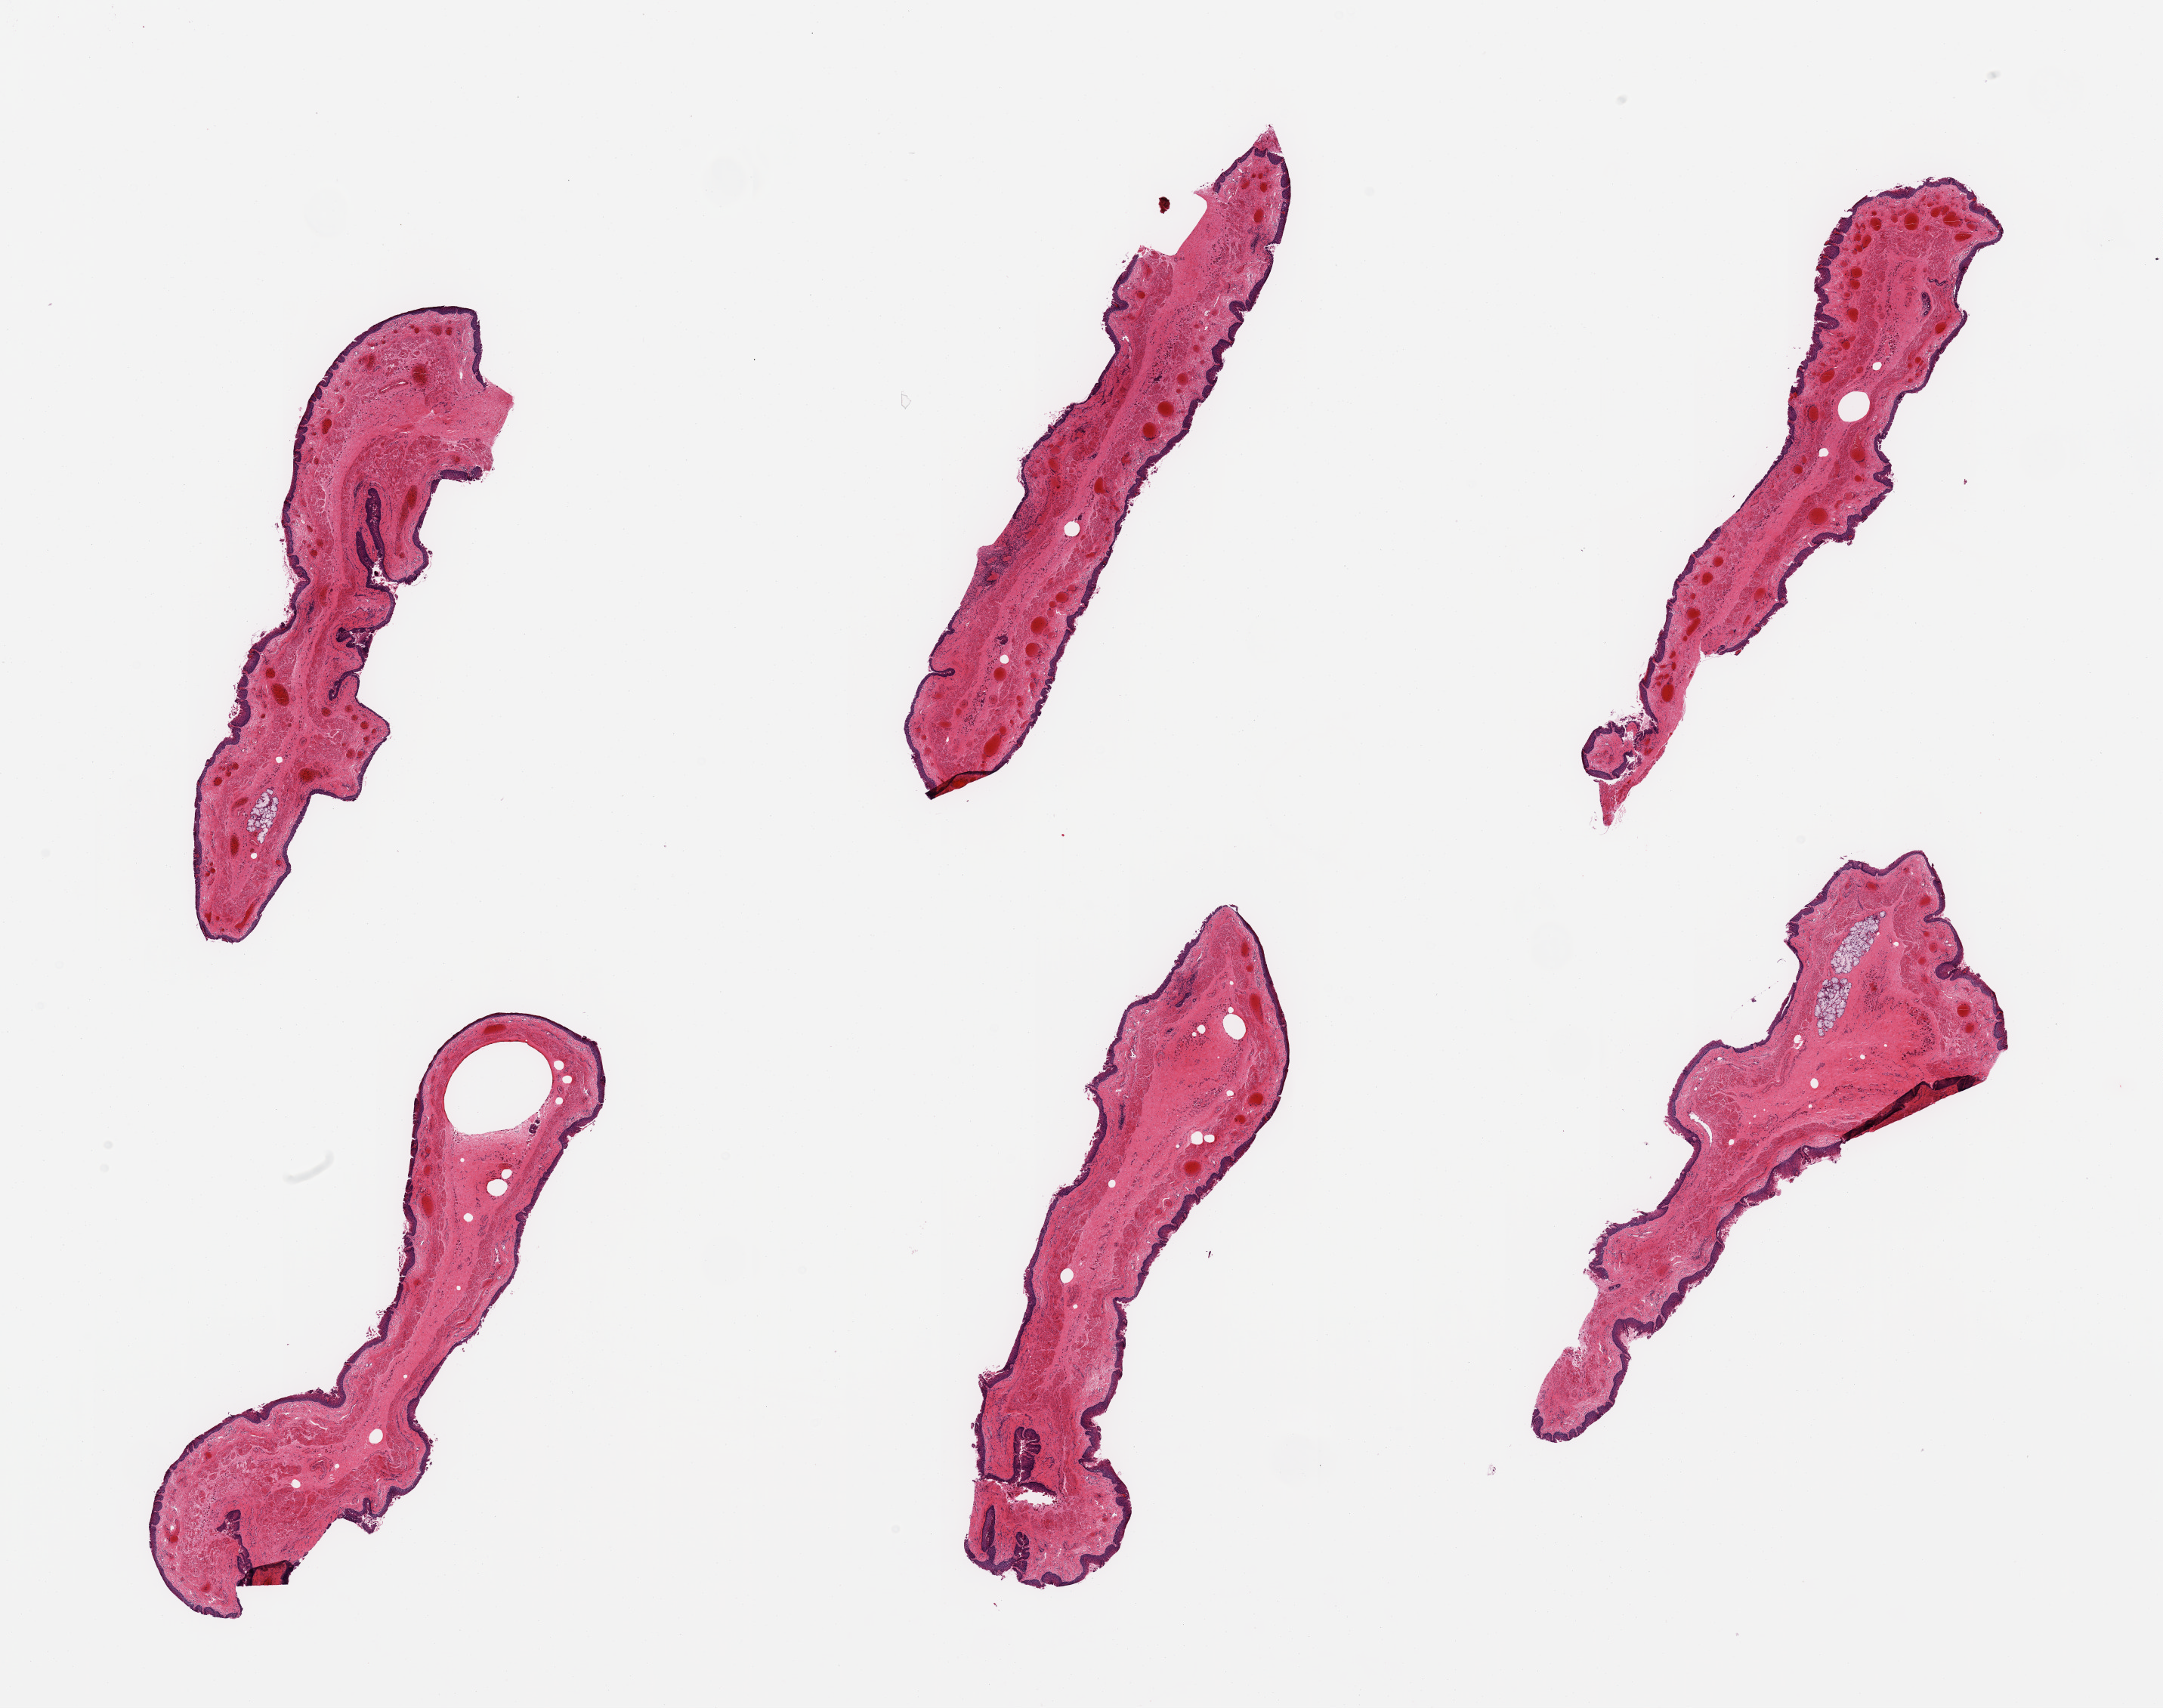
Digitized haematoxylin and eosin-stained section, brightfield, shown as a low-resolution overview of the whole scanned area (about 22.6 x 17.9 mm); PAXgene-fixed paraffin-embedded (PFPE) section; target tissue: esophageal mucous membrane; donor tissue sample.
- review note (as recorded): 6 pieces; squamous surface partially sloughed; round bubble-like submucosal artefactual defects